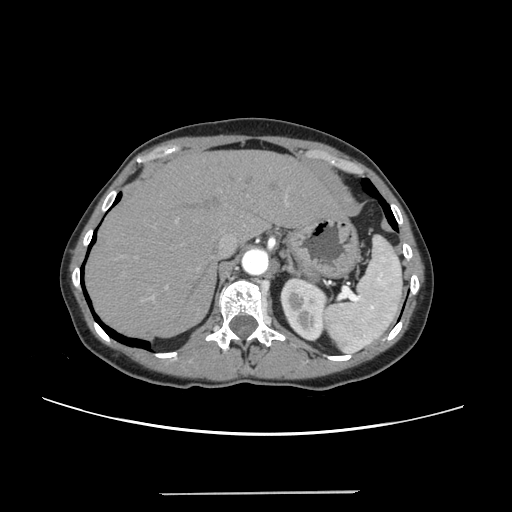
Contrast-enhanced abdominal CT, one axial slice. Slice 184 of 240 in the series (ordered by position). 120 kVp. Soft-tissue window (W 400 / L 40 HU). 512 × 512 image matrix, field of view 371 × 371 mm. Female patient, age 60 years. Case-level facts recorded for this patient, not image findings: diagnosis: colorectal cancer liver metastases, imaged before liver resection; multiple liver metastases: no; largest metastasis: 1.5 cm; disease in both lobes: no.
Outlined on this slice (manually delineated by an expert):
- hepatic veins: bounding box <220,234,237,254> (left, top, right, bottom; pixels)
- liver: <88,151,339,337>
- planned liver remnant (the part of the liver to remain after resection): <88,151,339,337>
- portal vein (with intrahepatic branches): <152,199,288,300>